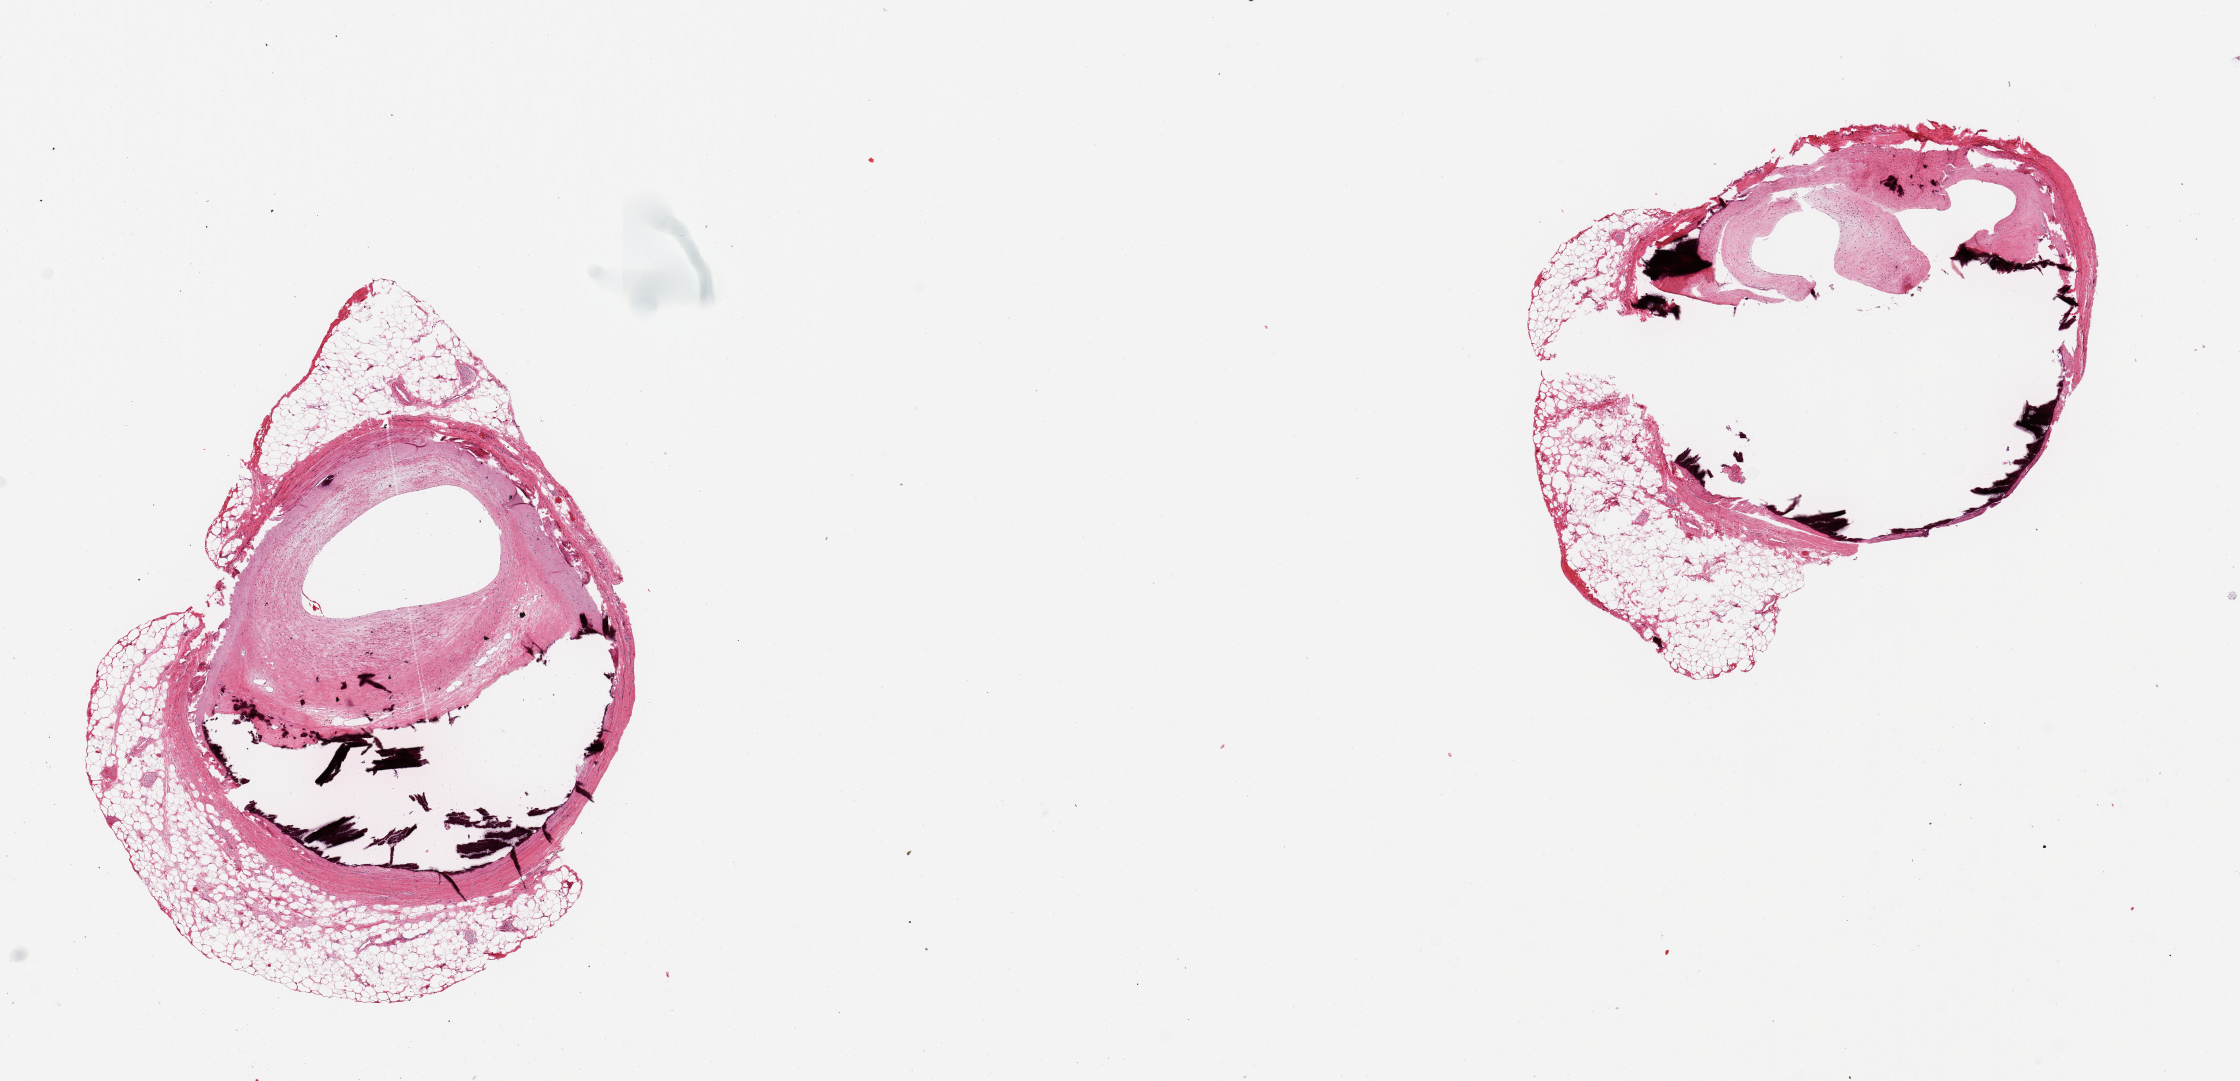
Digitized H&E-stained section, brightfield — low-resolution overview of the scanned area, about 17.7 x 8.6 mm, PAXgene-fixed, paraffin-embedded tissue, sampled site (target tissue): coronary artery, donor tissue sample.
Review note (as recorded): 2 pieces; fragmented, atherosclerotic plaque with calcification and luminal compromise; attached external fat over 1 mm.